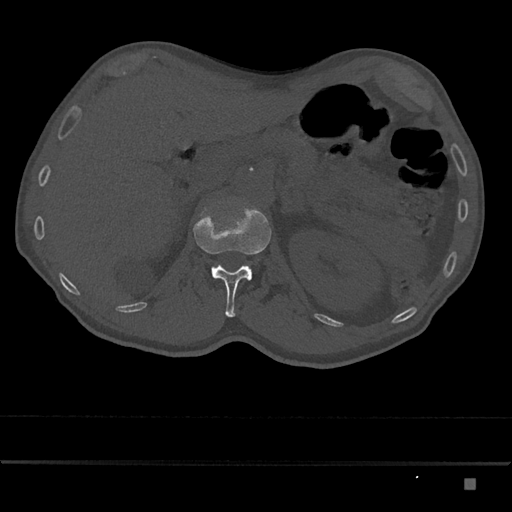
CT including the spine, one axial slice; position 536 of 797 along the scan axis; reconstruction kernel Br40s/3; 120 kVp; bone window (W 1800 / L 400 HU); 0.5 mm slice thickness; 512 × 512 image matrix, field of view 390 × 390 mm. Male patient, age 72 years. Case-level facts recorded for this patient, not image findings: primary cancer: prostate.
Annotated regions visible in this slice (semi-automatically segmented with operator editing):
- L1 vertebra: bounding box (x1, y1, x2, y2) in pixels: (193, 207, 272, 317)